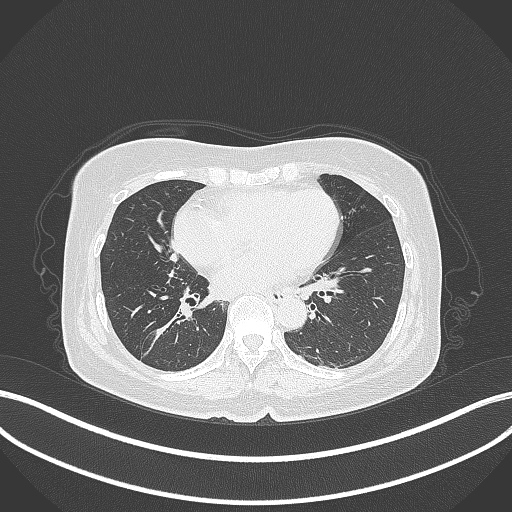
Chest CT, one axial slice. Slice 170 of 429 in the series (ordered by position). Reconstruction kernel B70f. 120 kVp. Lung window (W 1500 / L -600 HU). 1 mm slice thickness. 512 × 512 image matrix. Female patient, age 67 years. Case-level facts recorded for this patient, not image findings: clinical TNM (as recorded): T1c N1 M0; histopathological grade: G2-3.
Annotated regions visible in this slice (bounding box drawn by a radiologist):
- lung tumour (recorded histology: adenocarcinoma): bounding box (x1, y1, x2, y2) in pixels: (137, 303, 191, 357)